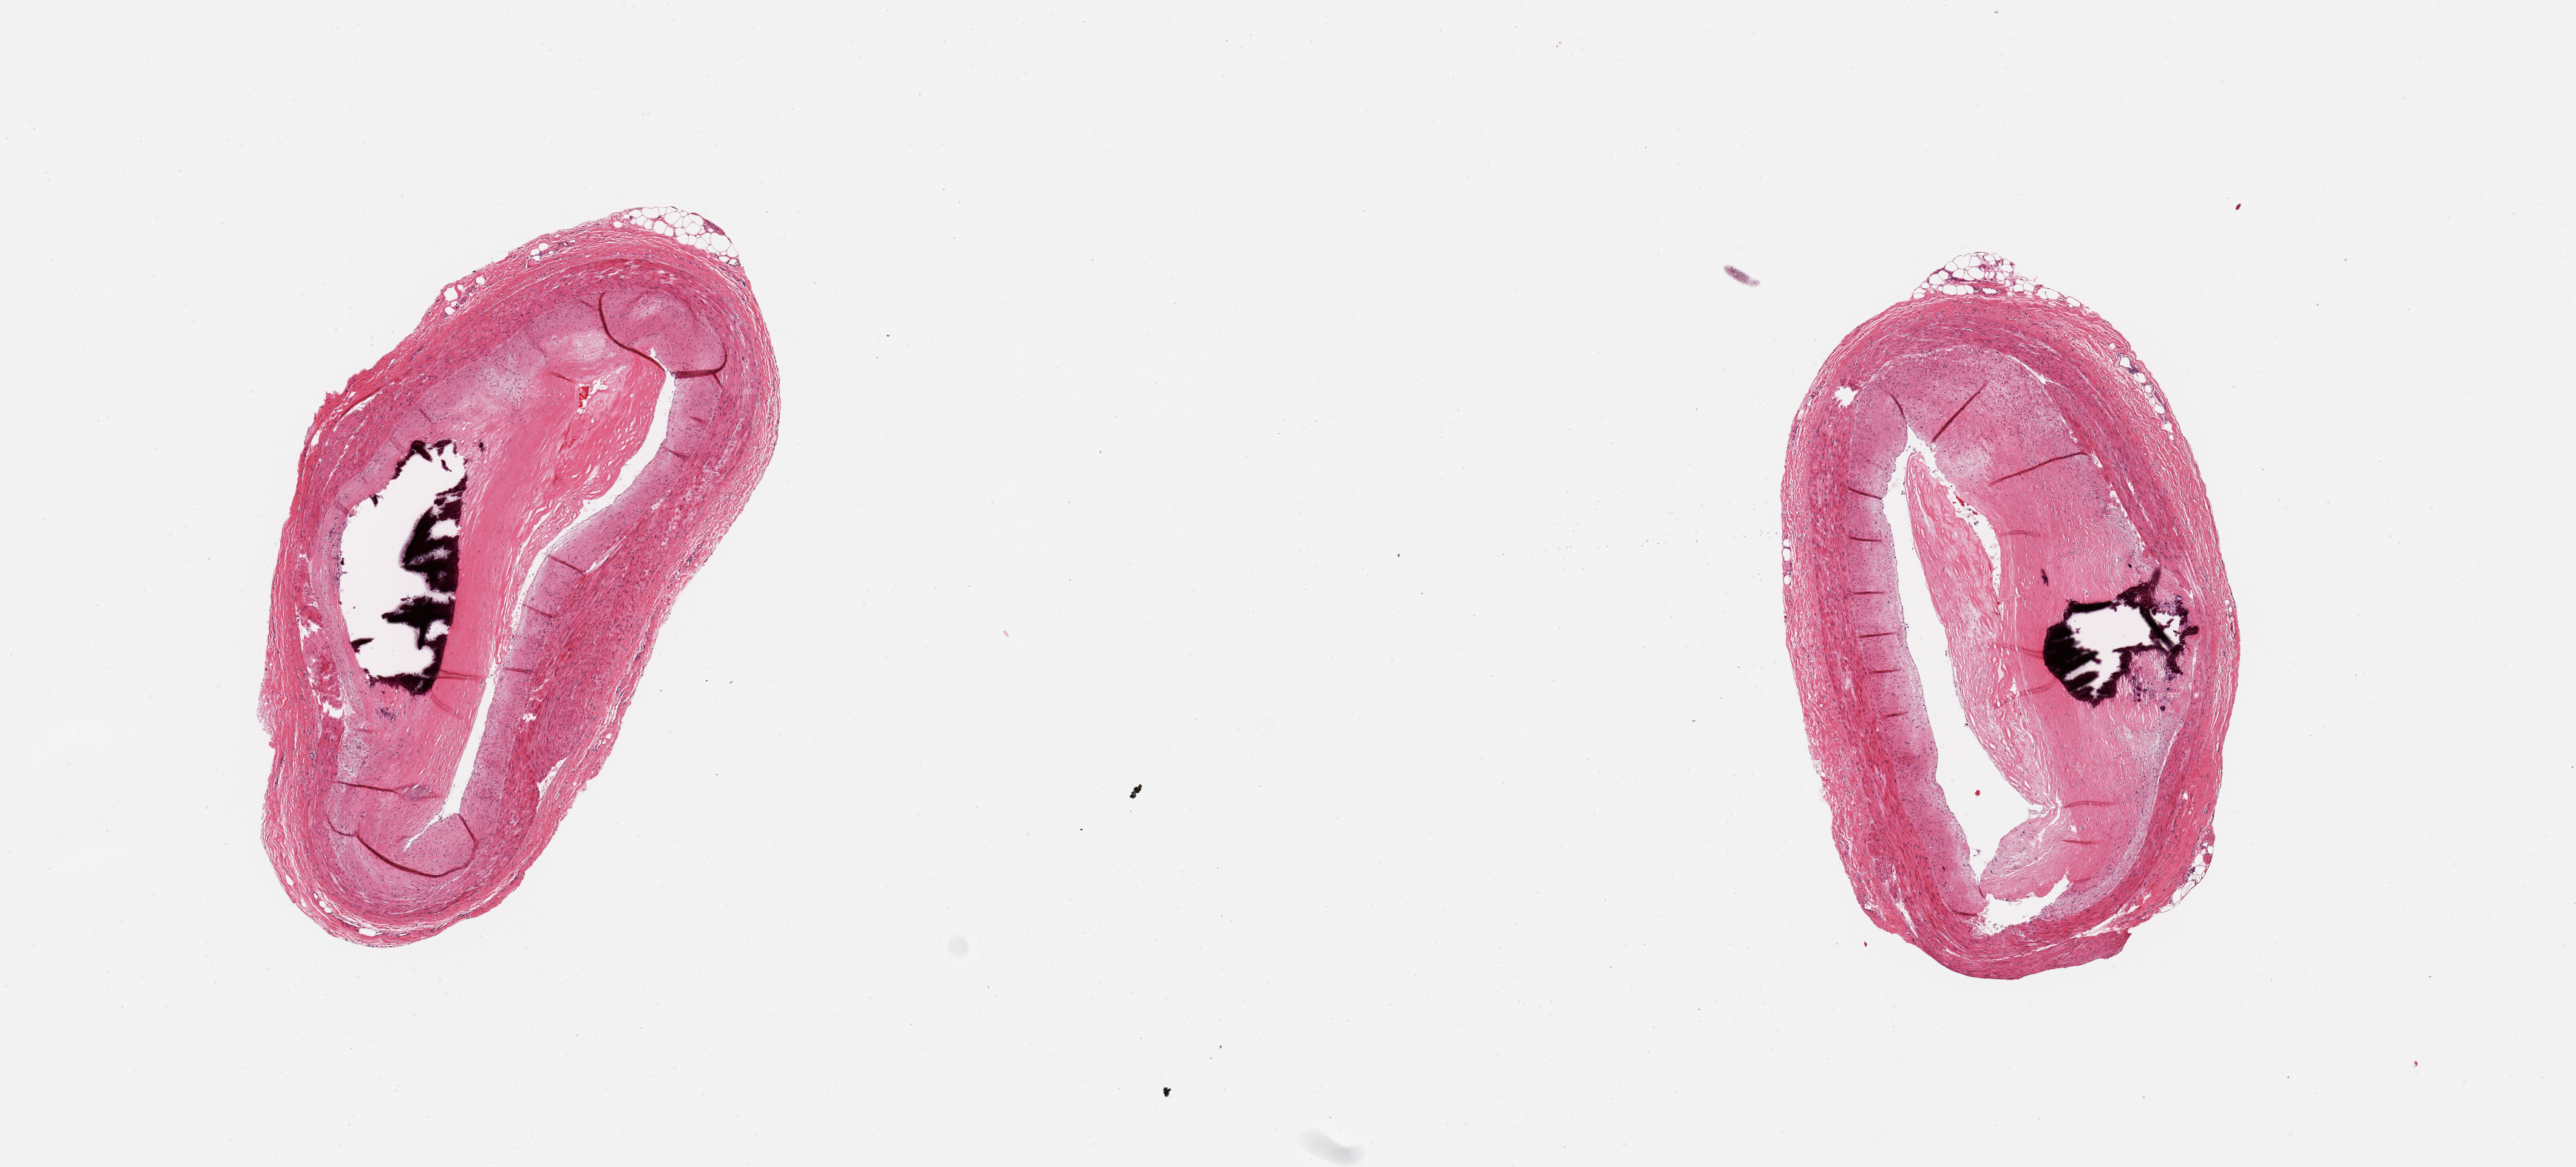
Digitized haematoxylin and eosin-stained section — whole scanned area (about 13.8 x 6.2 mm) shown as a low-resolution overview, PAXgene-fixed paraffin-embedded (PFPE) section, section of coronary artery (target tissue), tissue donor sample.
• pathologist's review note for this sample: 2 pieces; calcific atherosclerosis with profound luminal narrowing